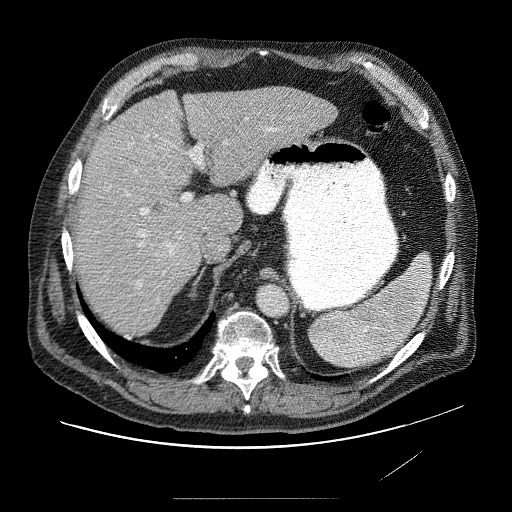
Contrast-enhanced abdominal CT (liver protocol), one axial slice; slice 54 of 89 in the series (ordered by position); reconstruction kernel STANDARD; 120 kVp; soft-tissue window (W 400 / L 40 HU); 512 × 512 image matrix, field of view 420 × 420 mm. From the clinical record (not read from this slice): diagnosis: hepatocellular carcinoma (patient treated with transarterial chemoembolisation; whether this scan precedes or follows treatment is not stated here); TNM stage (as recorded): Stage-IVA; Child-Pugh class: A.
Outlined on this slice (semi-automatic segmentation, software-assisted and operator-edited):
- abdominal aorta: box from (x=257, y=285) to (x=287, y=316) px
- liver parenchyma outside the tumour (the mass and vessels are separate outlines, so this box may not span the whole liver): (x=76, y=86)–(x=340, y=324)
- mass: (x=138, y=97)–(x=197, y=185)
- liver vessels: (x=104, y=124)–(x=310, y=286)